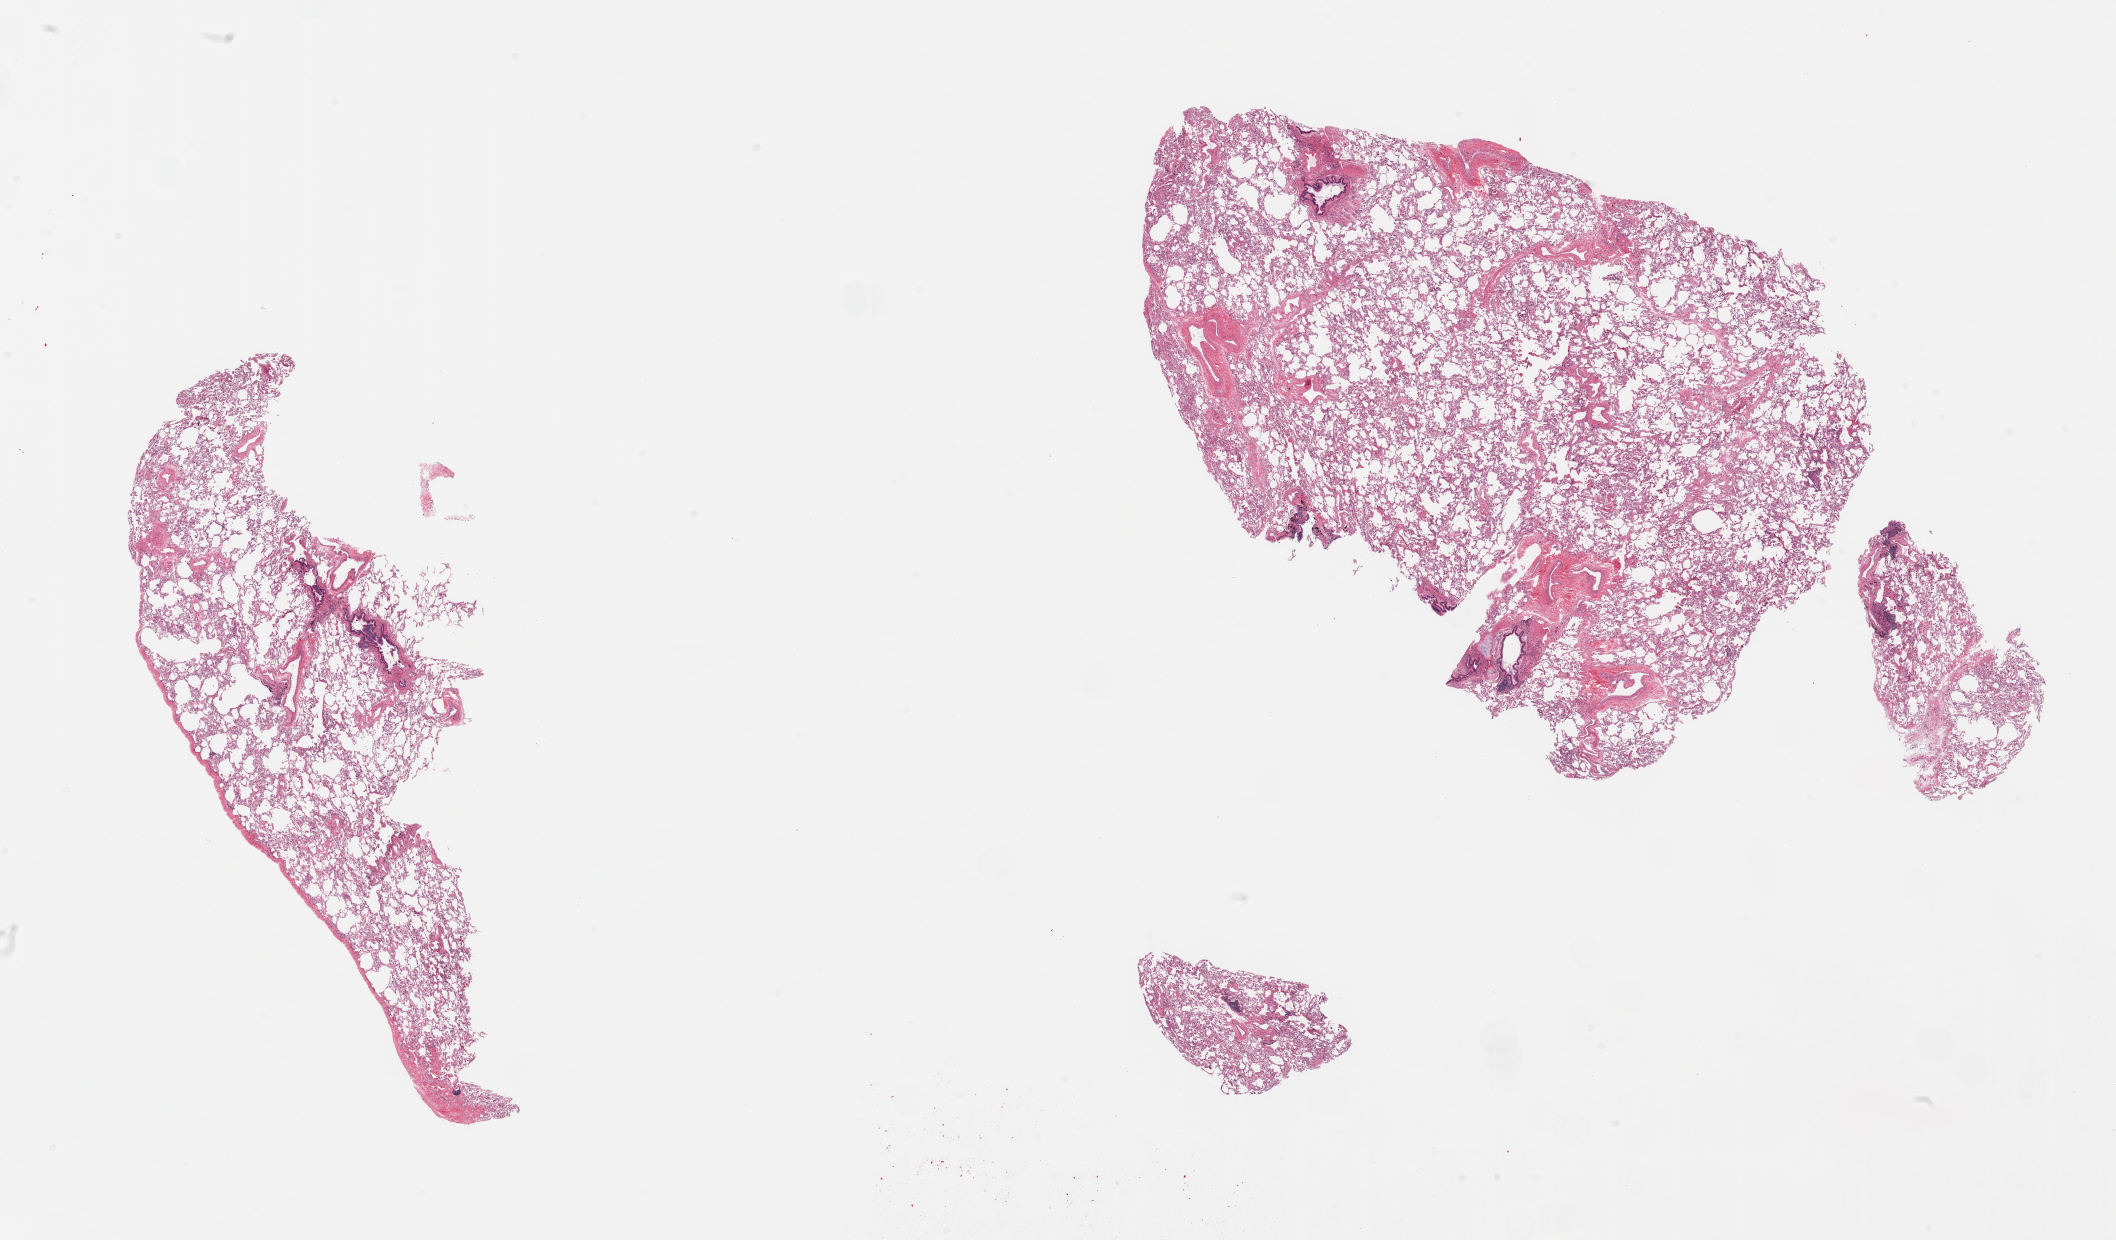
Whole-slide image, H&E stain, low-resolution overview of the scanned area, about 33.5 x 19.6 mm (acquisition: 20x scan), PAXgene-fixed, paraffin-embedded tissue, target tissue: lung, tissue donor sample. Female donor.
Pathologist's review note for this sample: 2 pieces, minimal edema/congestion.